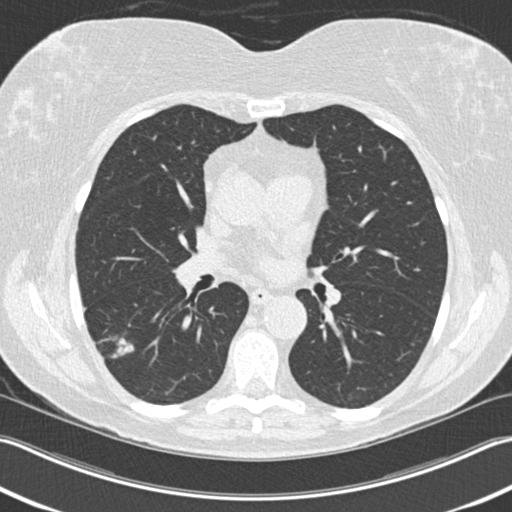
Chest CT (low-dose screening protocol), one axial image; first (baseline) screen; lung window (W 1500 / L -600 HU); 2 mm slice thickness; standard (soft-tissue) reconstruction kernel (B30f). Female participant, aged 63 years at enrolment. Current smoker at enrolment.
- Expert-annotated lung lesion, bounding box [x1, y1, x2, y2] px = [88, 321, 146, 372].
- The screening reader recorded 3 non-calcified nodules or masses ≥4 mm on this exam (right upper lobe, right lower lobe, right lower lobe); which of them this box marks is not recorded.
- Later outcome: lung cancer diagnosed 57 days after this screen — bronchiolo-alveolar adenocarcinoma, NOS, right lower lobe, well differentiated (G1), stage IA (AJCC 6th edition), 25 mm at pathology.